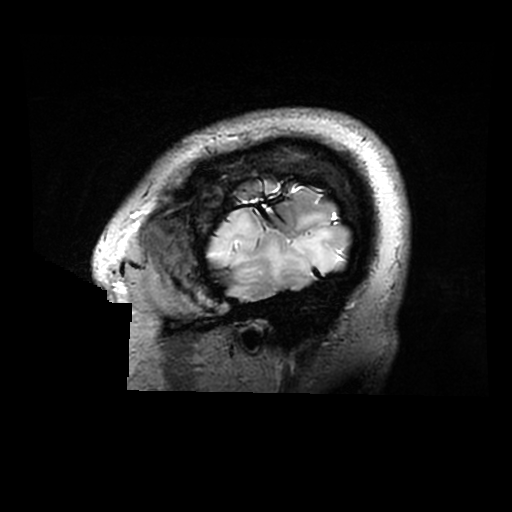
Brain MRI from a brain-tumour surgery series, one sagittal slice. Slice 254 of 320 in the series (ordered by position). 0.6 mm slice thickness. 512 × 512 image matrix, field of view 240 × 240 mm. Case-level facts recorded for this patient, not image findings: histopathology: Astrocytoma; WHO grade: 2; IDH mutation: yes.
Structures marked on this image (manually delineated by an expert):
- tumour: bounding box [x1, y1, x2, y2] px = [208, 209, 347, 283]